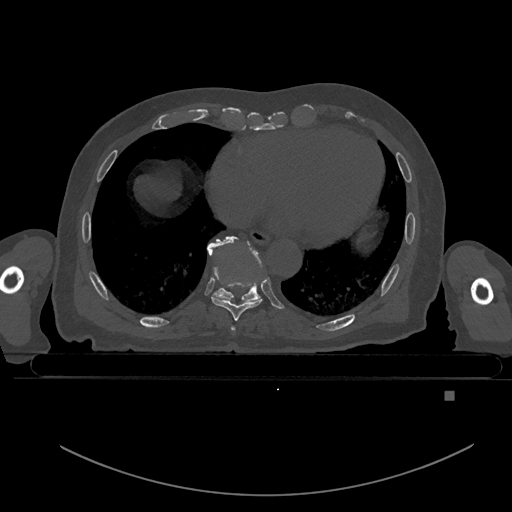
CT including the spine, one axial slice. Slice 182 of 969 in the series (ordered by position). Bone window (W 1800 / L 400 HU). 0.5 mm slice thickness. 512 × 512 image matrix, field of view 456 × 456 mm. Patient: male, 82 years. Case-level facts recorded for this patient, not image findings: primary cancer: prostate.
Outlined on this slice (semi-automatically segmented with operator editing):
- T7 vertebra: bounding box [x1, y1, x2, y2] px = [231, 326, 235, 332]
- T8 vertebra: [212, 262, 262, 321]
- T9 vertebra: [207, 236, 262, 302]